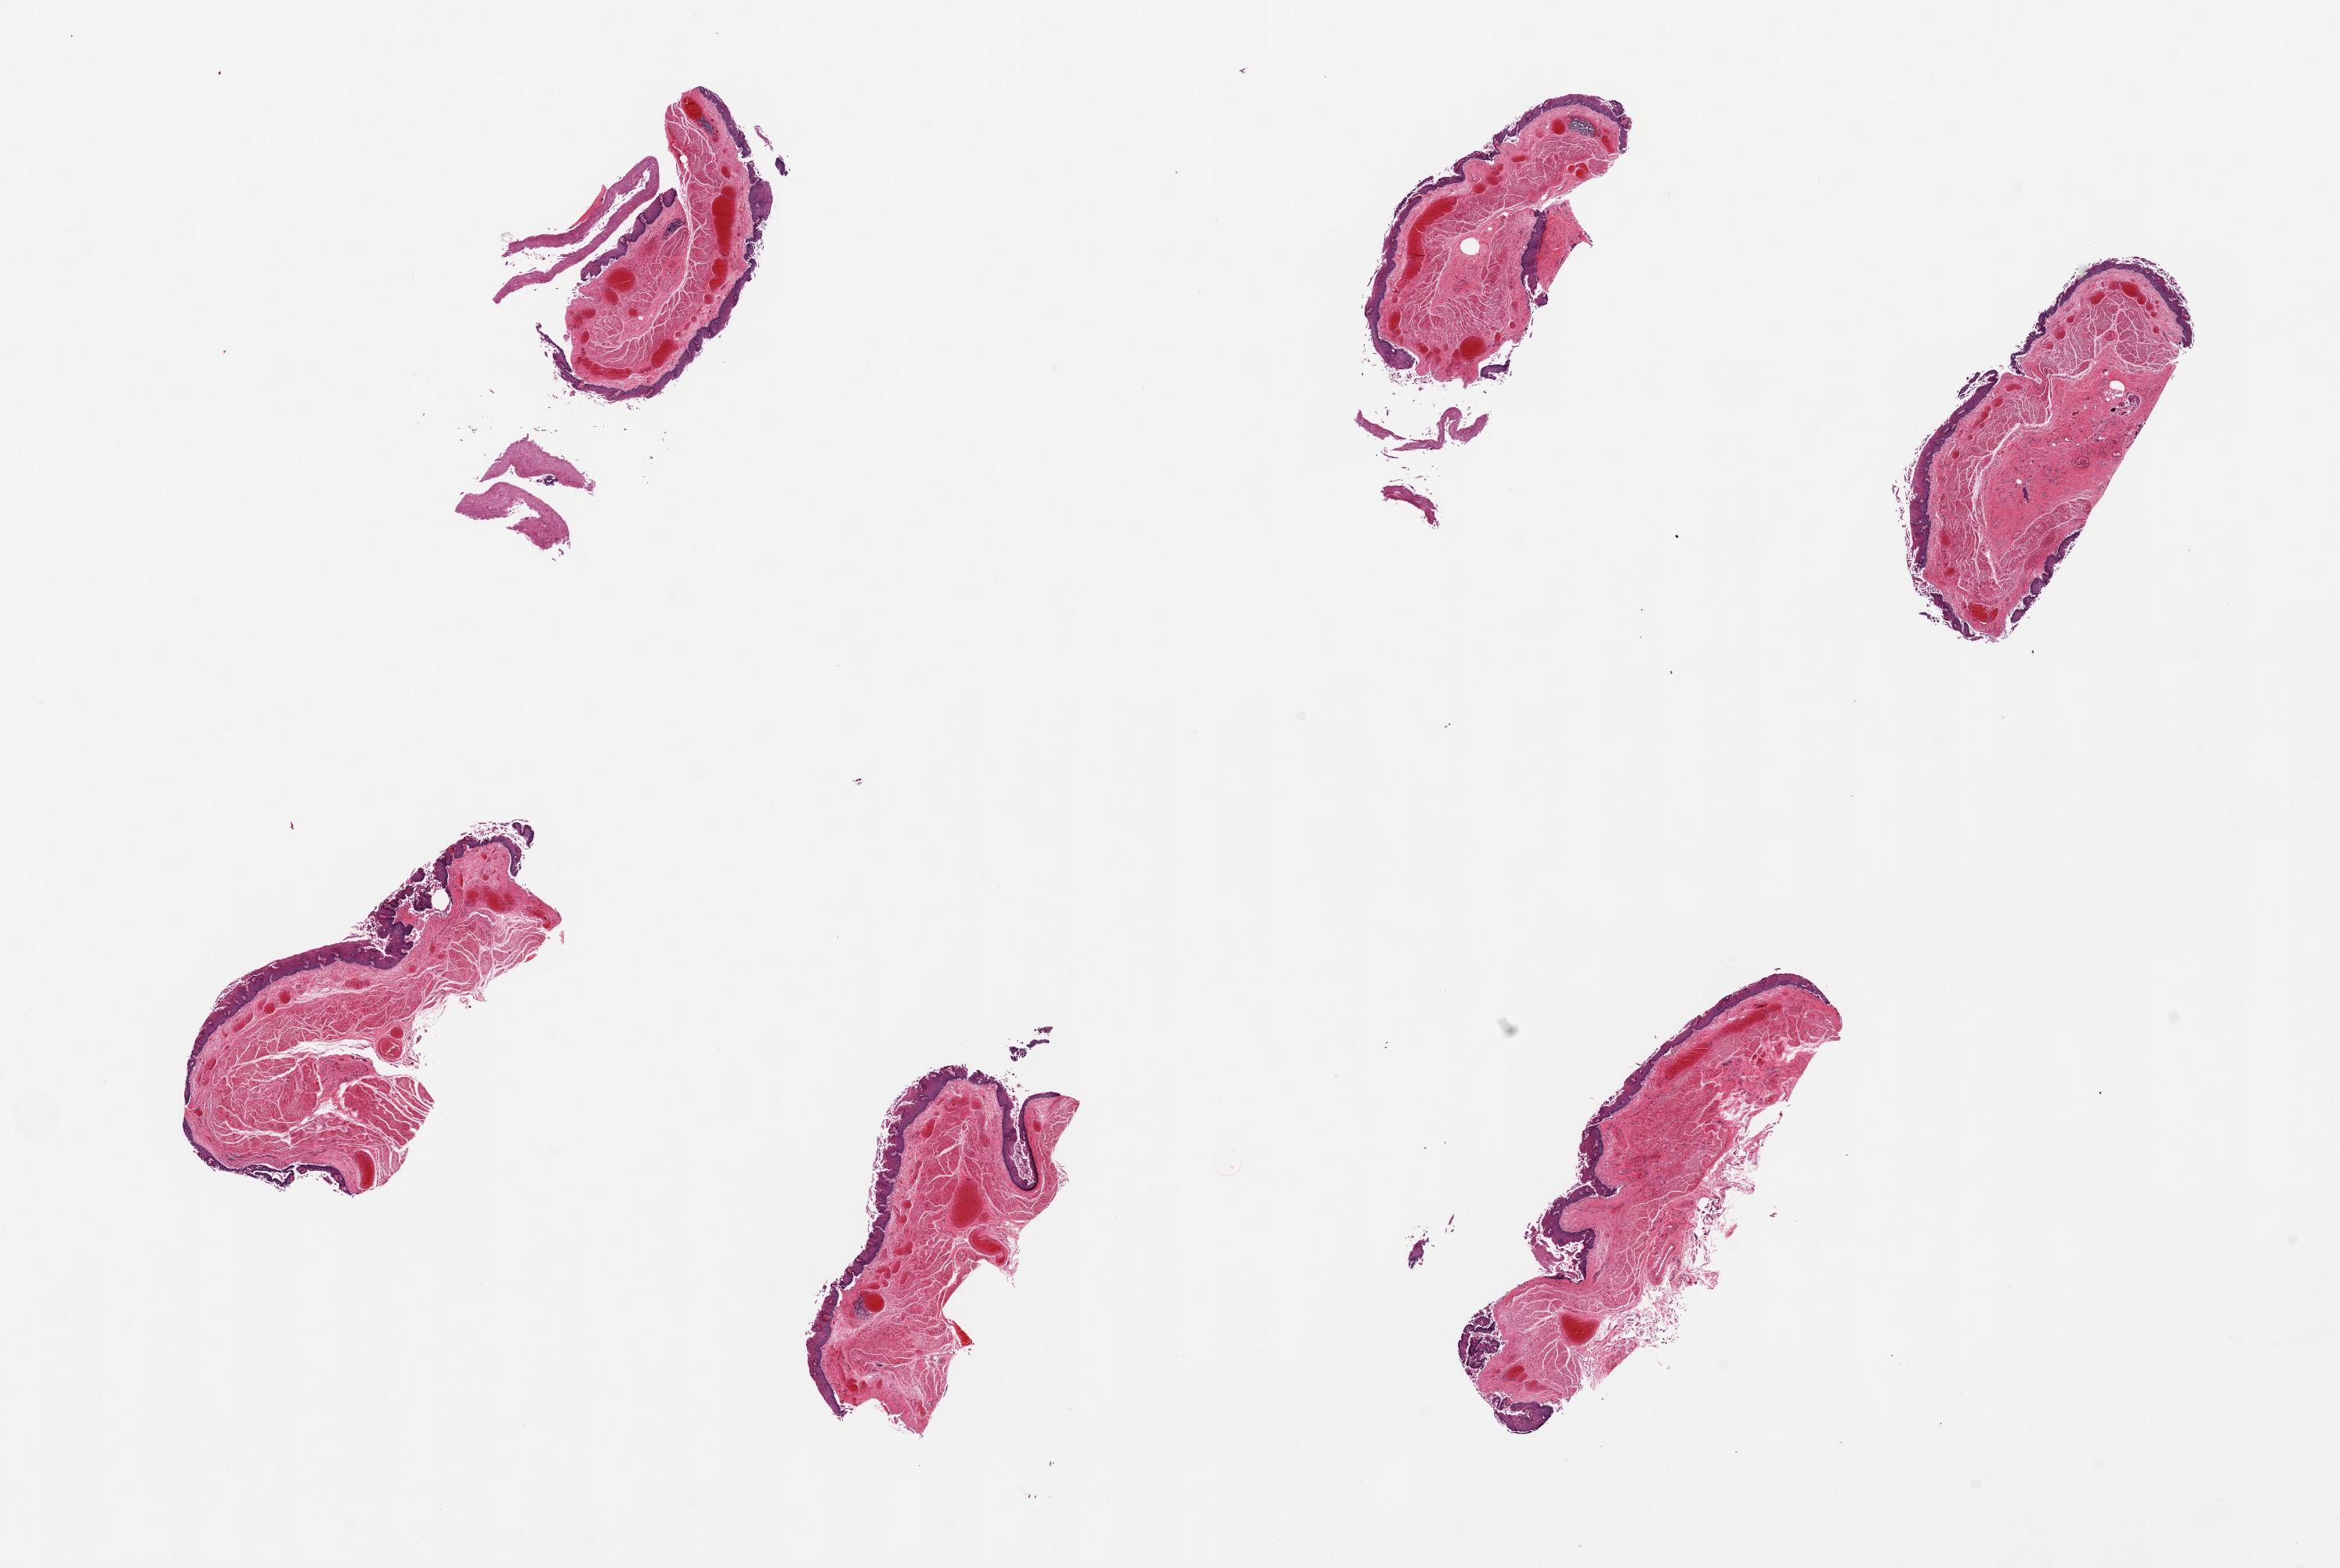
Whole-slide image, H&E stain, brightfield, whole scanned area (about 23.6 x 15.8 mm, from a 20x scan) shown as a low-resolution overview. PAXgene-fixed, paraffin-embedded tissue. Section of esophageal mucous membrane (target tissue). Tissue donor sample. Donor sex: male.
* reviewer comment on this tissue sample: 6 pieces; squamous desquamation